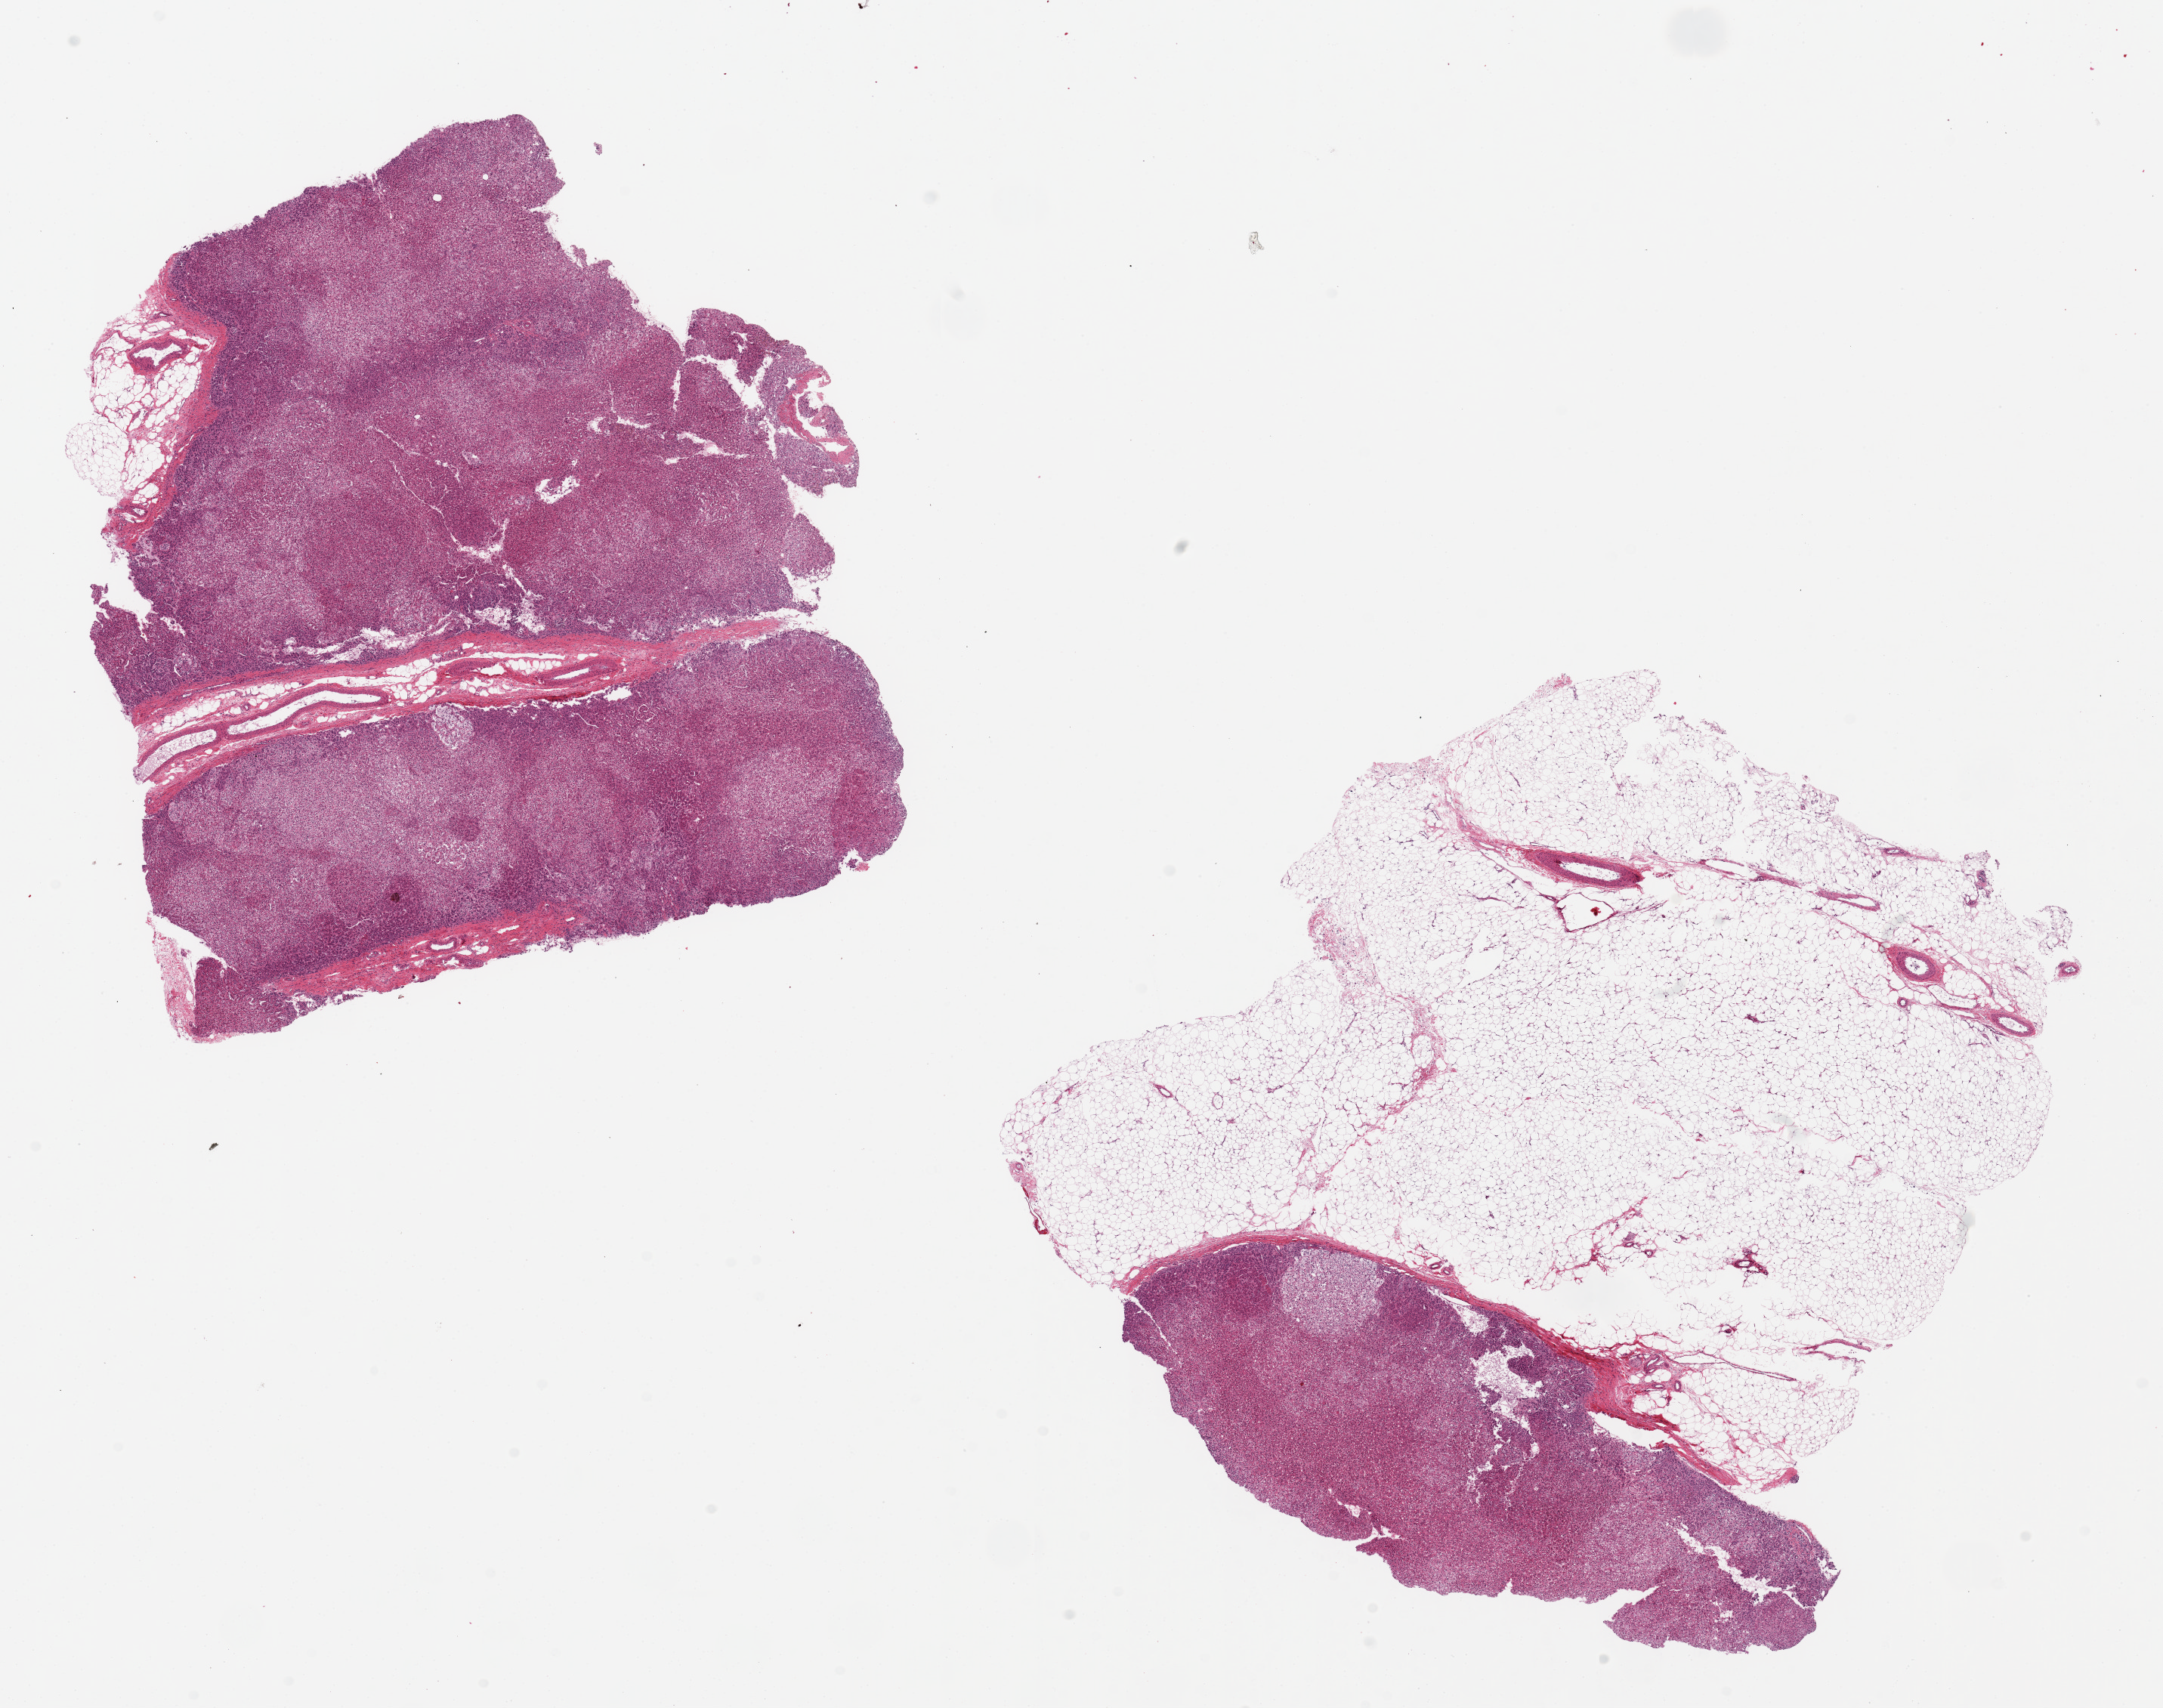
Digitized H&E-stained section — whole scanned area (about 22.6 x 17.9 mm) shown as a low-resolution overview, PAXgene-fixed, paraffin-embedded tissue, target tissue: adrenal gland, donor tissue sample. Male donor.
Reviewer comment on this tissue sample: 2 pieces one 8.5x7; one 8x2mm aliquot, all cortex. Smaller has attached ~7x7mm nubbin of fat.